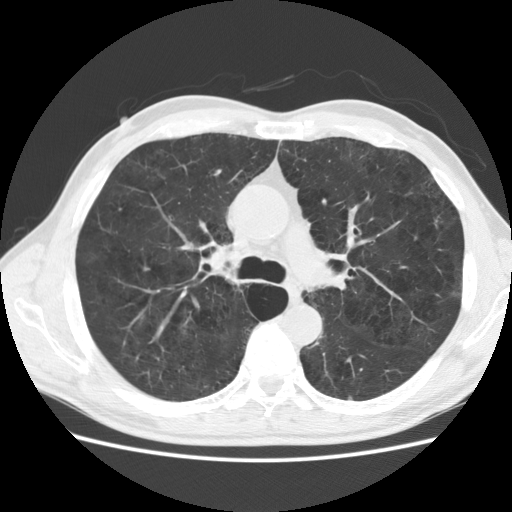
Chest CT (low-dose screening protocol), one axial image. Baseline annual screen. Lung window (W 1500 / L -600 HU). 2.5 mm slice thickness. Standard (soft-tissue) reconstruction kernel (STANDARD). Slice 68 of 177 in the series. 512 × 512 image matrix, field of view 360 × 360 mm. Male, age 58 years at enrolment. Current smoker at enrolment.
Lesion marked by an expert reader, bounding box <420,211,457,237> (left, top, right, bottom; pixels). Screening reader's record for this exam: no non-calcified nodule ≥4 mm recorded. Official screen result: negative screen, minor abnormalities not suspicious for lung cancer. Participant outcome: lung cancer diagnosed 832 days after this screen (after the third annual screen) — adenocarcinoma, NOS, left upper lobe, stage IA (AJCC 6th edition), 9 mm at pathology.